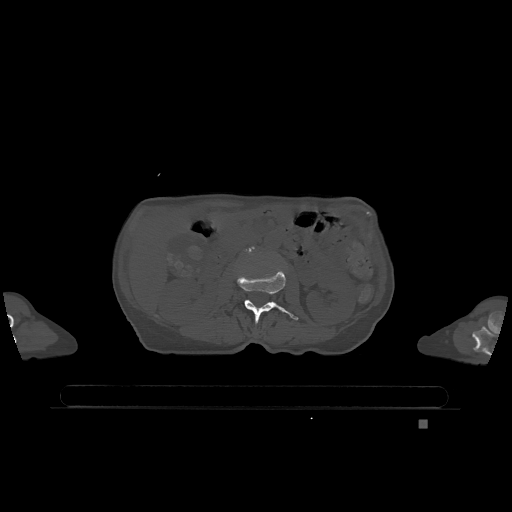
CT including the spine, one axial slice. Slice 408 of 1317 in the series (ordered by position). Bone window (W 1800 / L 400 HU). 0.5 mm slice thickness. 512 × 512 image matrix, field of view 500 × 500 mm. Patient: female, 74 years. From the clinical record (not read from this slice): primary cancer: lung; vertebrae with lytic lesions (as recorded): T1, T4, T5, T6, L4, L5.
Annotated regions visible in this slice (semi-automatically segmented with operator editing):
- L2 vertebra: bounding box <237,269,299,324> (left, top, right, bottom; pixels)
- L3 vertebra: <250,247,254,250>